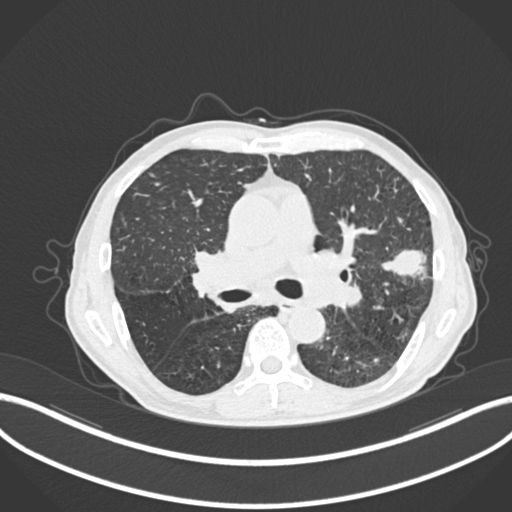
Chest CT, one axial slice. Position 145 of 287 along the scan axis. Reconstruction kernel B30f. Lung window (W 1500 / L -600 HU). 1 mm slice thickness. 512 × 512 image matrix, field of view 400 × 400 mm. Male patient, age 74 years. Case-level facts recorded for this patient, not image findings: clinical TNM (as recorded): T2a N1 M0.
Outlined on this slice (rectangle marked by the reading radiologist):
- lung tumour (recorded histology: adenocarcinoma): bounding box [x1, y1, x2, y2] px = [381, 249, 430, 282]